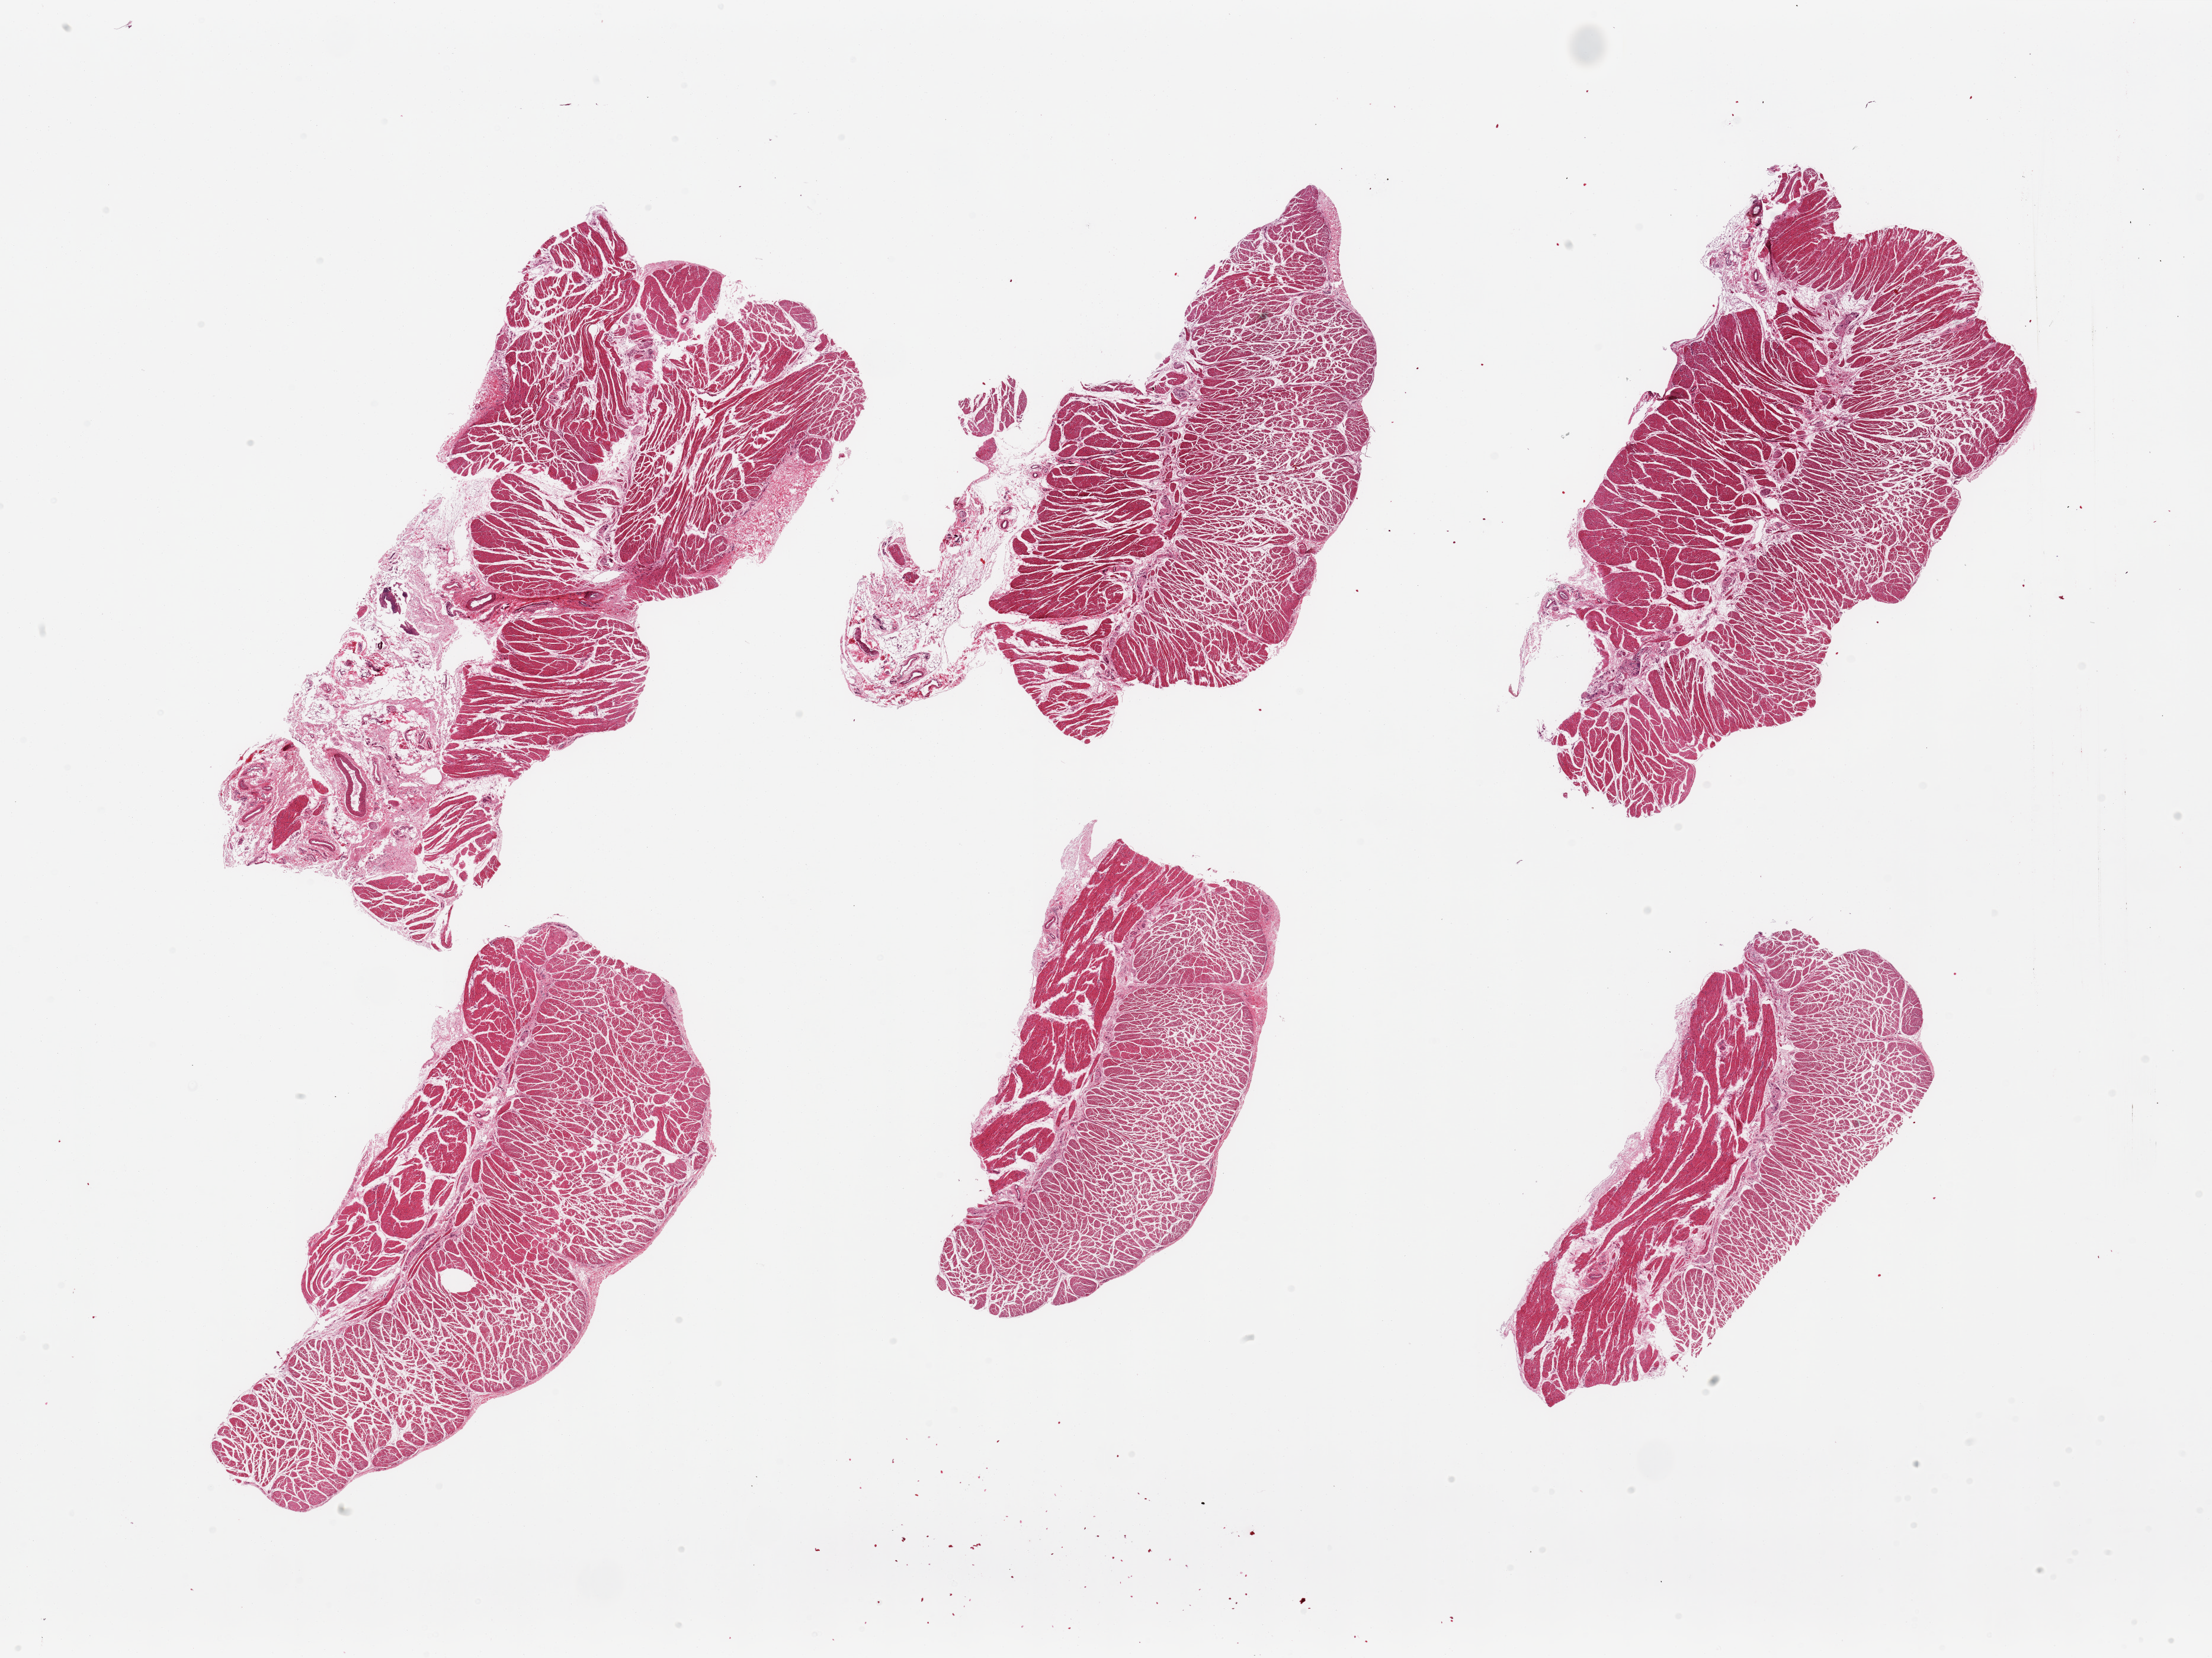
Whole-slide image, H&E stain, brightfield — a low-resolution overview of the entire scanned area, about 29.5 x 22.1 mm. PAXgene-fixed paraffin-embedded (PFPE) section. Target tissue: esophageal muscle. Tissue donor sample. Donor: female.
• review note (as recorded): 6 pieces; well trimmed except for 2 pieces with 30% submucosa